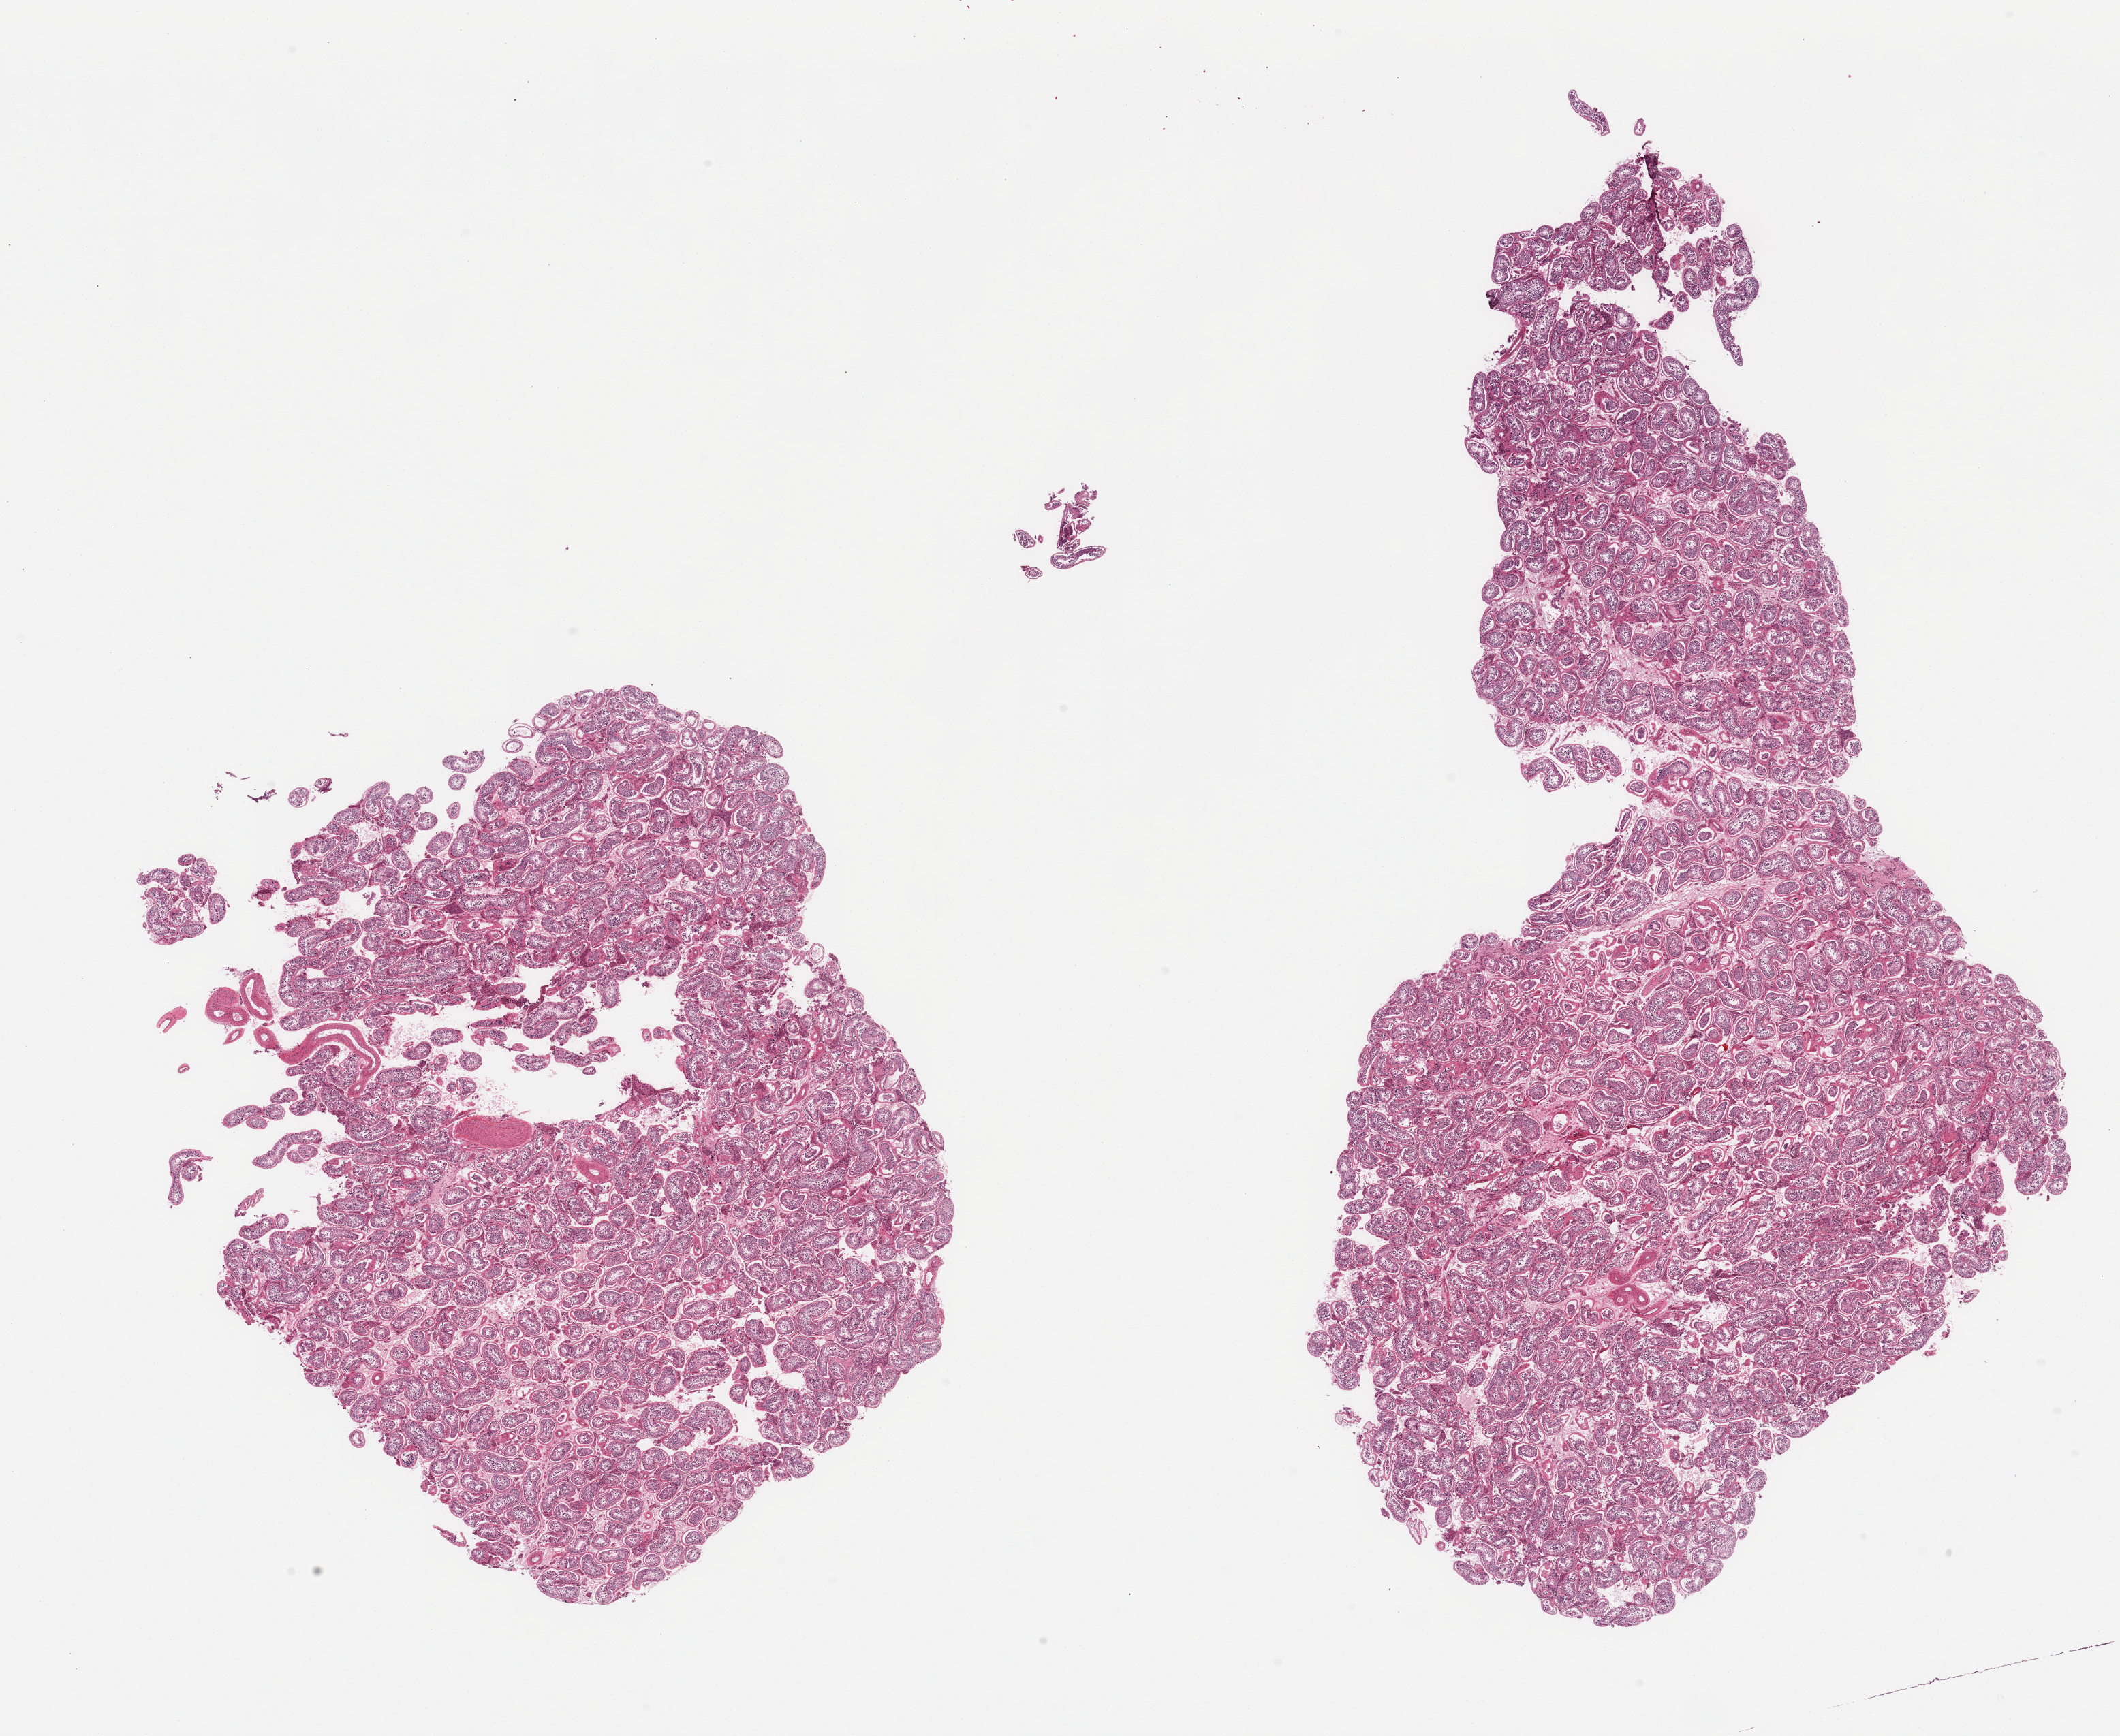
Haematoxylin and eosin whole-slide image, brightfield — shown as a low-resolution overview of the whole scanned area (about 24.6 x 20.2 mm), PAXgene-fixed paraffin-embedded (PFPE) section, target tissue: testis, donor tissue sample.
- reviewer comment on this tissue sample: 2 pieces; active spermatogenesis